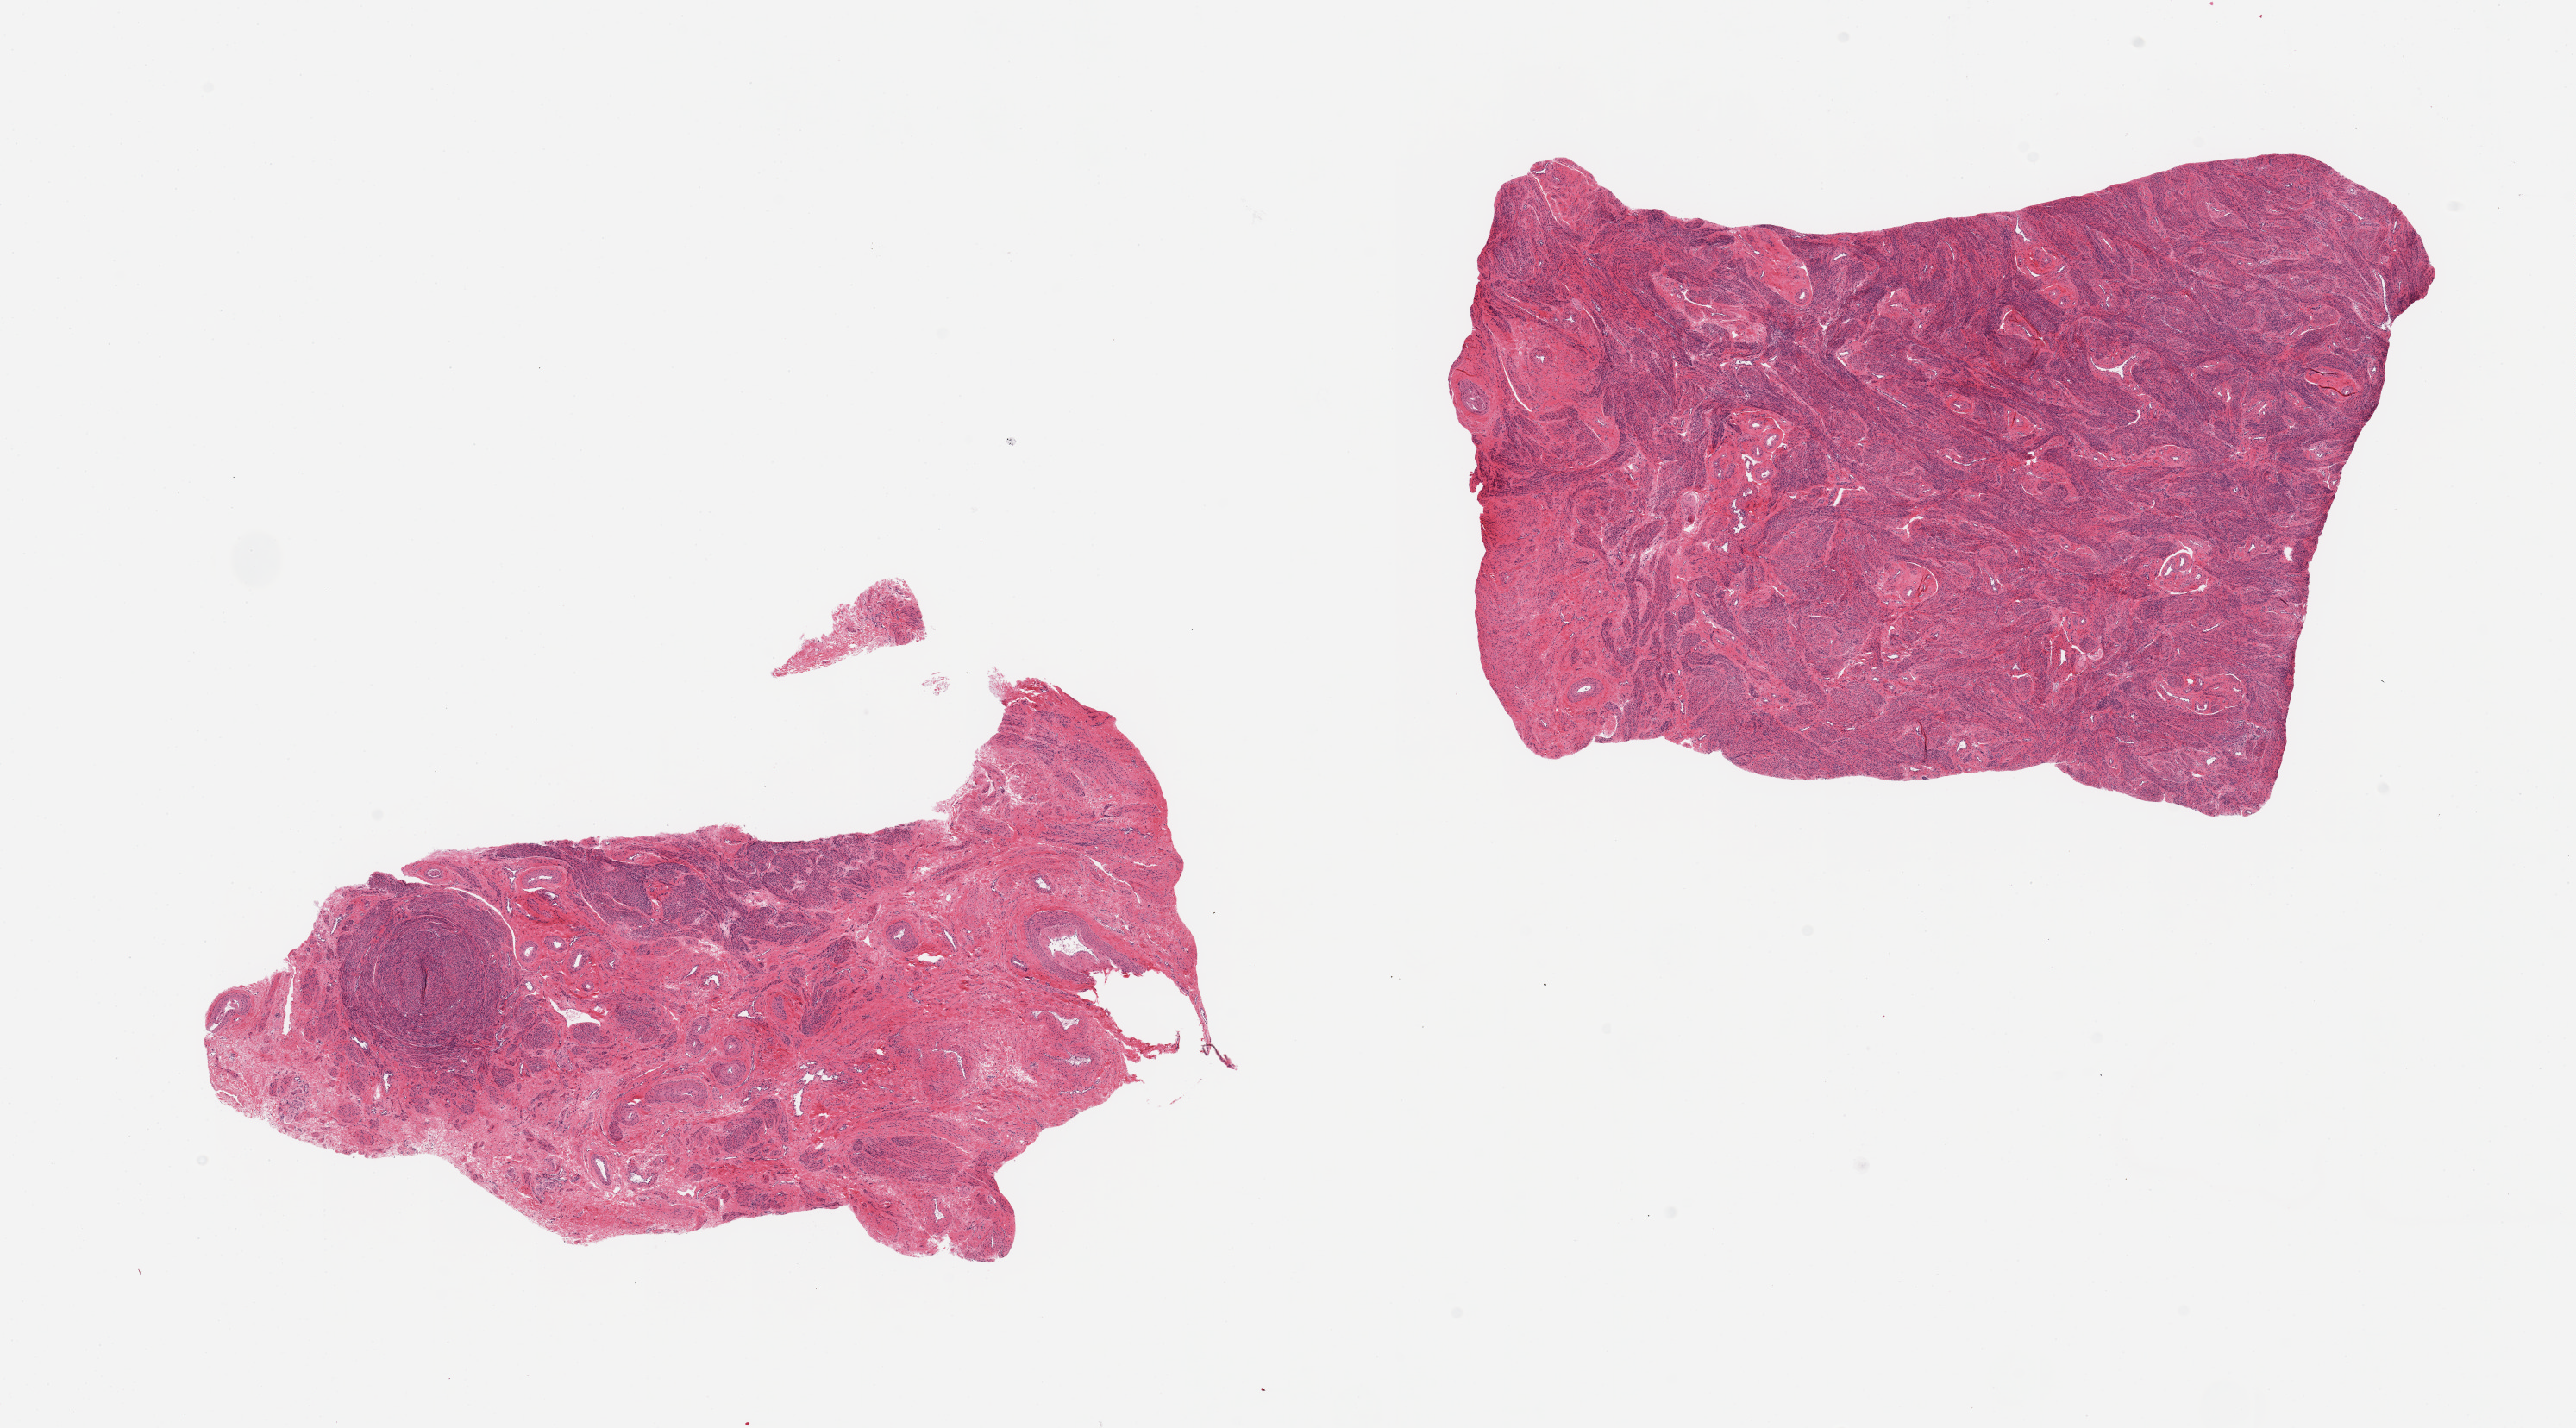
Hematoxylin and eosin (H&E) whole-slide image — low-resolution overview of the scanned area, about 23.6 x 13.1 mm (slide scanned at 20x). PAXgene-fixed paraffin-embedded (PFPE) section. Section of uterus (target tissue). Donor tissue sample. Female donor.
Reviewer comment on this tissue sample: 2 pieces; myometrium only (in this cut).